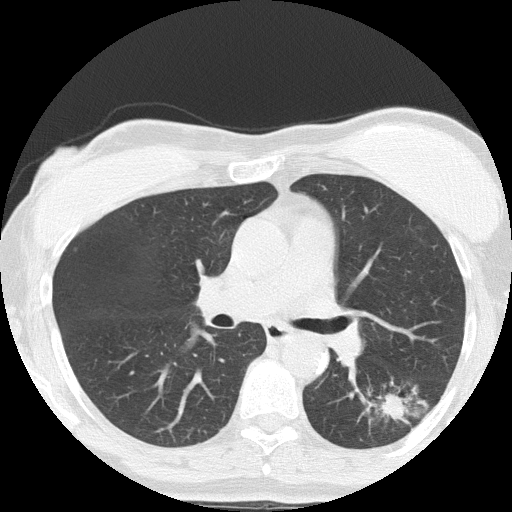
Axial slice from a low-dose chest CT screening exam, third screening round (two years after baseline), lung window (W 1500 / L -600 HU), 2 mm slice thickness, slice 65 of 152 in the series. Female participant, aged 64 years at enrolment. Former smoker at enrolment.
- Expert reader's lesion annotation, bounding box (x1, y1, x2, y2) in pixels: (358, 374, 447, 447).
- The screening reader recorded 3 non-calcified nodules or masses ≥4 mm on this exam (right upper lobe, left lower lobe, right middle lobe); which of them this box marks is not recorded.
- Official screen result: positive, other.
- Later outcome: lung cancer diagnosed 212 days after this screen — adenocarcinoma, NOS, left lower lobe, moderately differentiated (G2), stage IA (AJCC 6th edition), 17 mm at pathology.